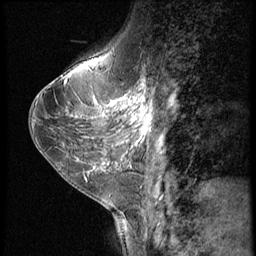
Breast MRI (dynamic contrast-enhanced), one sagittal slice; dynamic contrast-enhanced series, image 2 of 3 at this slice position (ordered by acquisition); 1.5 T; TE 4.2 ms, TR 9 ms; 2.5 mm slice thickness; 256 × 256 image matrix. Female patient, age 38 years. From the clinical record (not read from this slice): setting: breast cancer imaged before/during neoadjuvant chemotherapy; receptor status: triple-negative.
Annotated regions visible in this slice (semi-automatically segmented with operator editing):
- analysis volume of interest (the breast-tissue region the enhancement analysis was run in; not a lesion): bounding box [x1, y1, x2, y2] px = [107, 95, 159, 149]
- tumour enhancement mask (voxels above the 140 % enhancement threshold inside the analysis volume of interest): [110, 95, 151, 133]